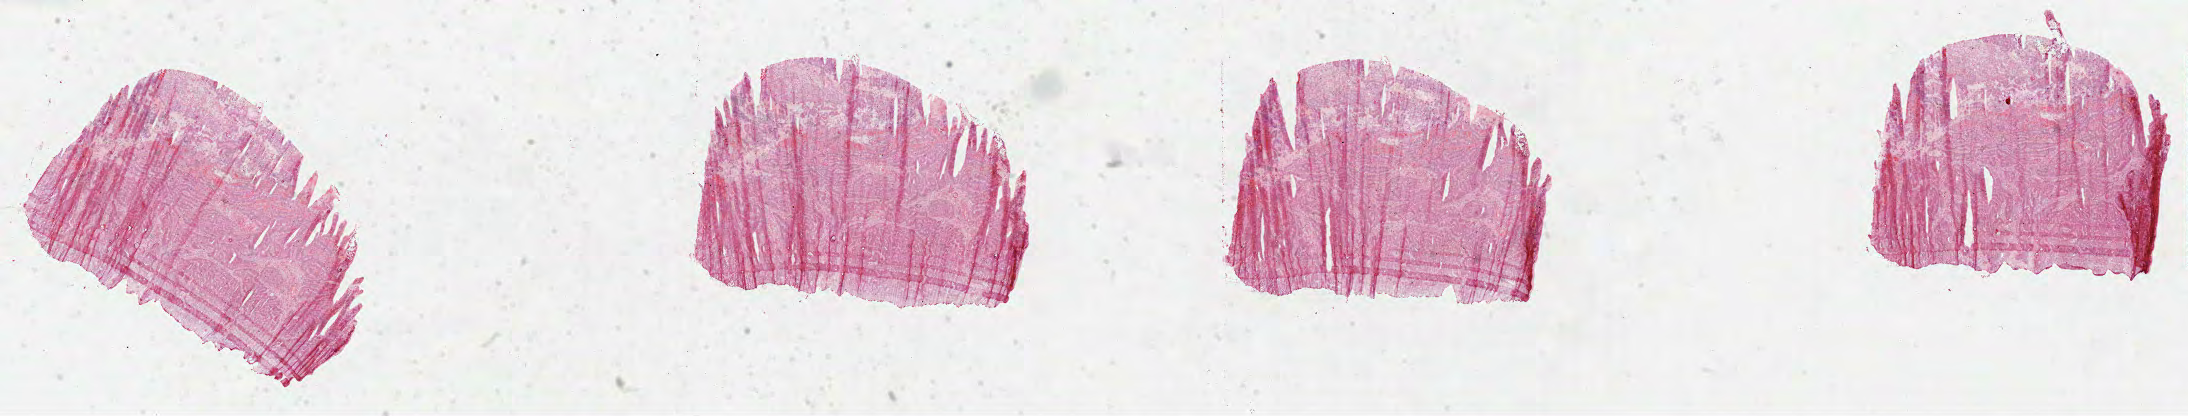
Digitized H&E tissue section (whole slide) — whole scanned area (about 35.3 x 6.7 mm, slide scanned at 40x) shown as a low-resolution overview. Formalin-fixed paraffin-embedded (FFPE) diagnostic section. Colon, primary tumour sample. Male patient; age at initial diagnosis 76 years.
Diagnosis: Adenocarcinoma, NOS (sigmoid colon).